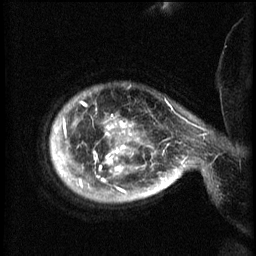
Breast MRI (dynamic contrast-enhanced), one sagittal slice; slice 53 of 60 in the series (ordered by position); 3 images stored at this slice position (order not interpretable as contrast timing); 1.5 T; TE 4.2 ms, TR 8.2 ms; 2.3 mm slice thickness; 256 × 256 image matrix, field of view 200 × 200 mm. Patient: female, 50 years.
Annotated regions visible in this slice (semi-automatically segmented with operator editing):
- analysis volume of interest (the breast-tissue region the enhancement analysis was run in; not a lesion): box from (x=52, y=88) to (x=169, y=203) px
- tumour enhancement mask (voxels above the 70 % enhancement threshold inside the analysis volume of interest): (x=52, y=102)–(x=169, y=193)